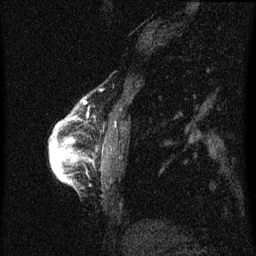
Breast MRI (dynamic contrast-enhanced), one sagittal slice. Slice 11 of 60 in the series (ordered by position). Dynamic contrast-enhanced series, image 2 of 3 at this slice position (ordered by acquisition). 1.5 T. TE 4.2 ms, TR 8 ms. 2 mm slice thickness. 256 × 256 image matrix. Patient: female, 56 years.
Structures marked on this image (semi-automatically segmented with operator editing):
- analysis volume of interest (the breast-tissue region the enhancement analysis was run in; not a lesion): bounding box [x1, y1, x2, y2] px = [50, 110, 79, 183]
- tumour enhancement mask (voxels above the 70 % enhancement threshold inside the analysis volume of interest): [50, 134, 77, 181]